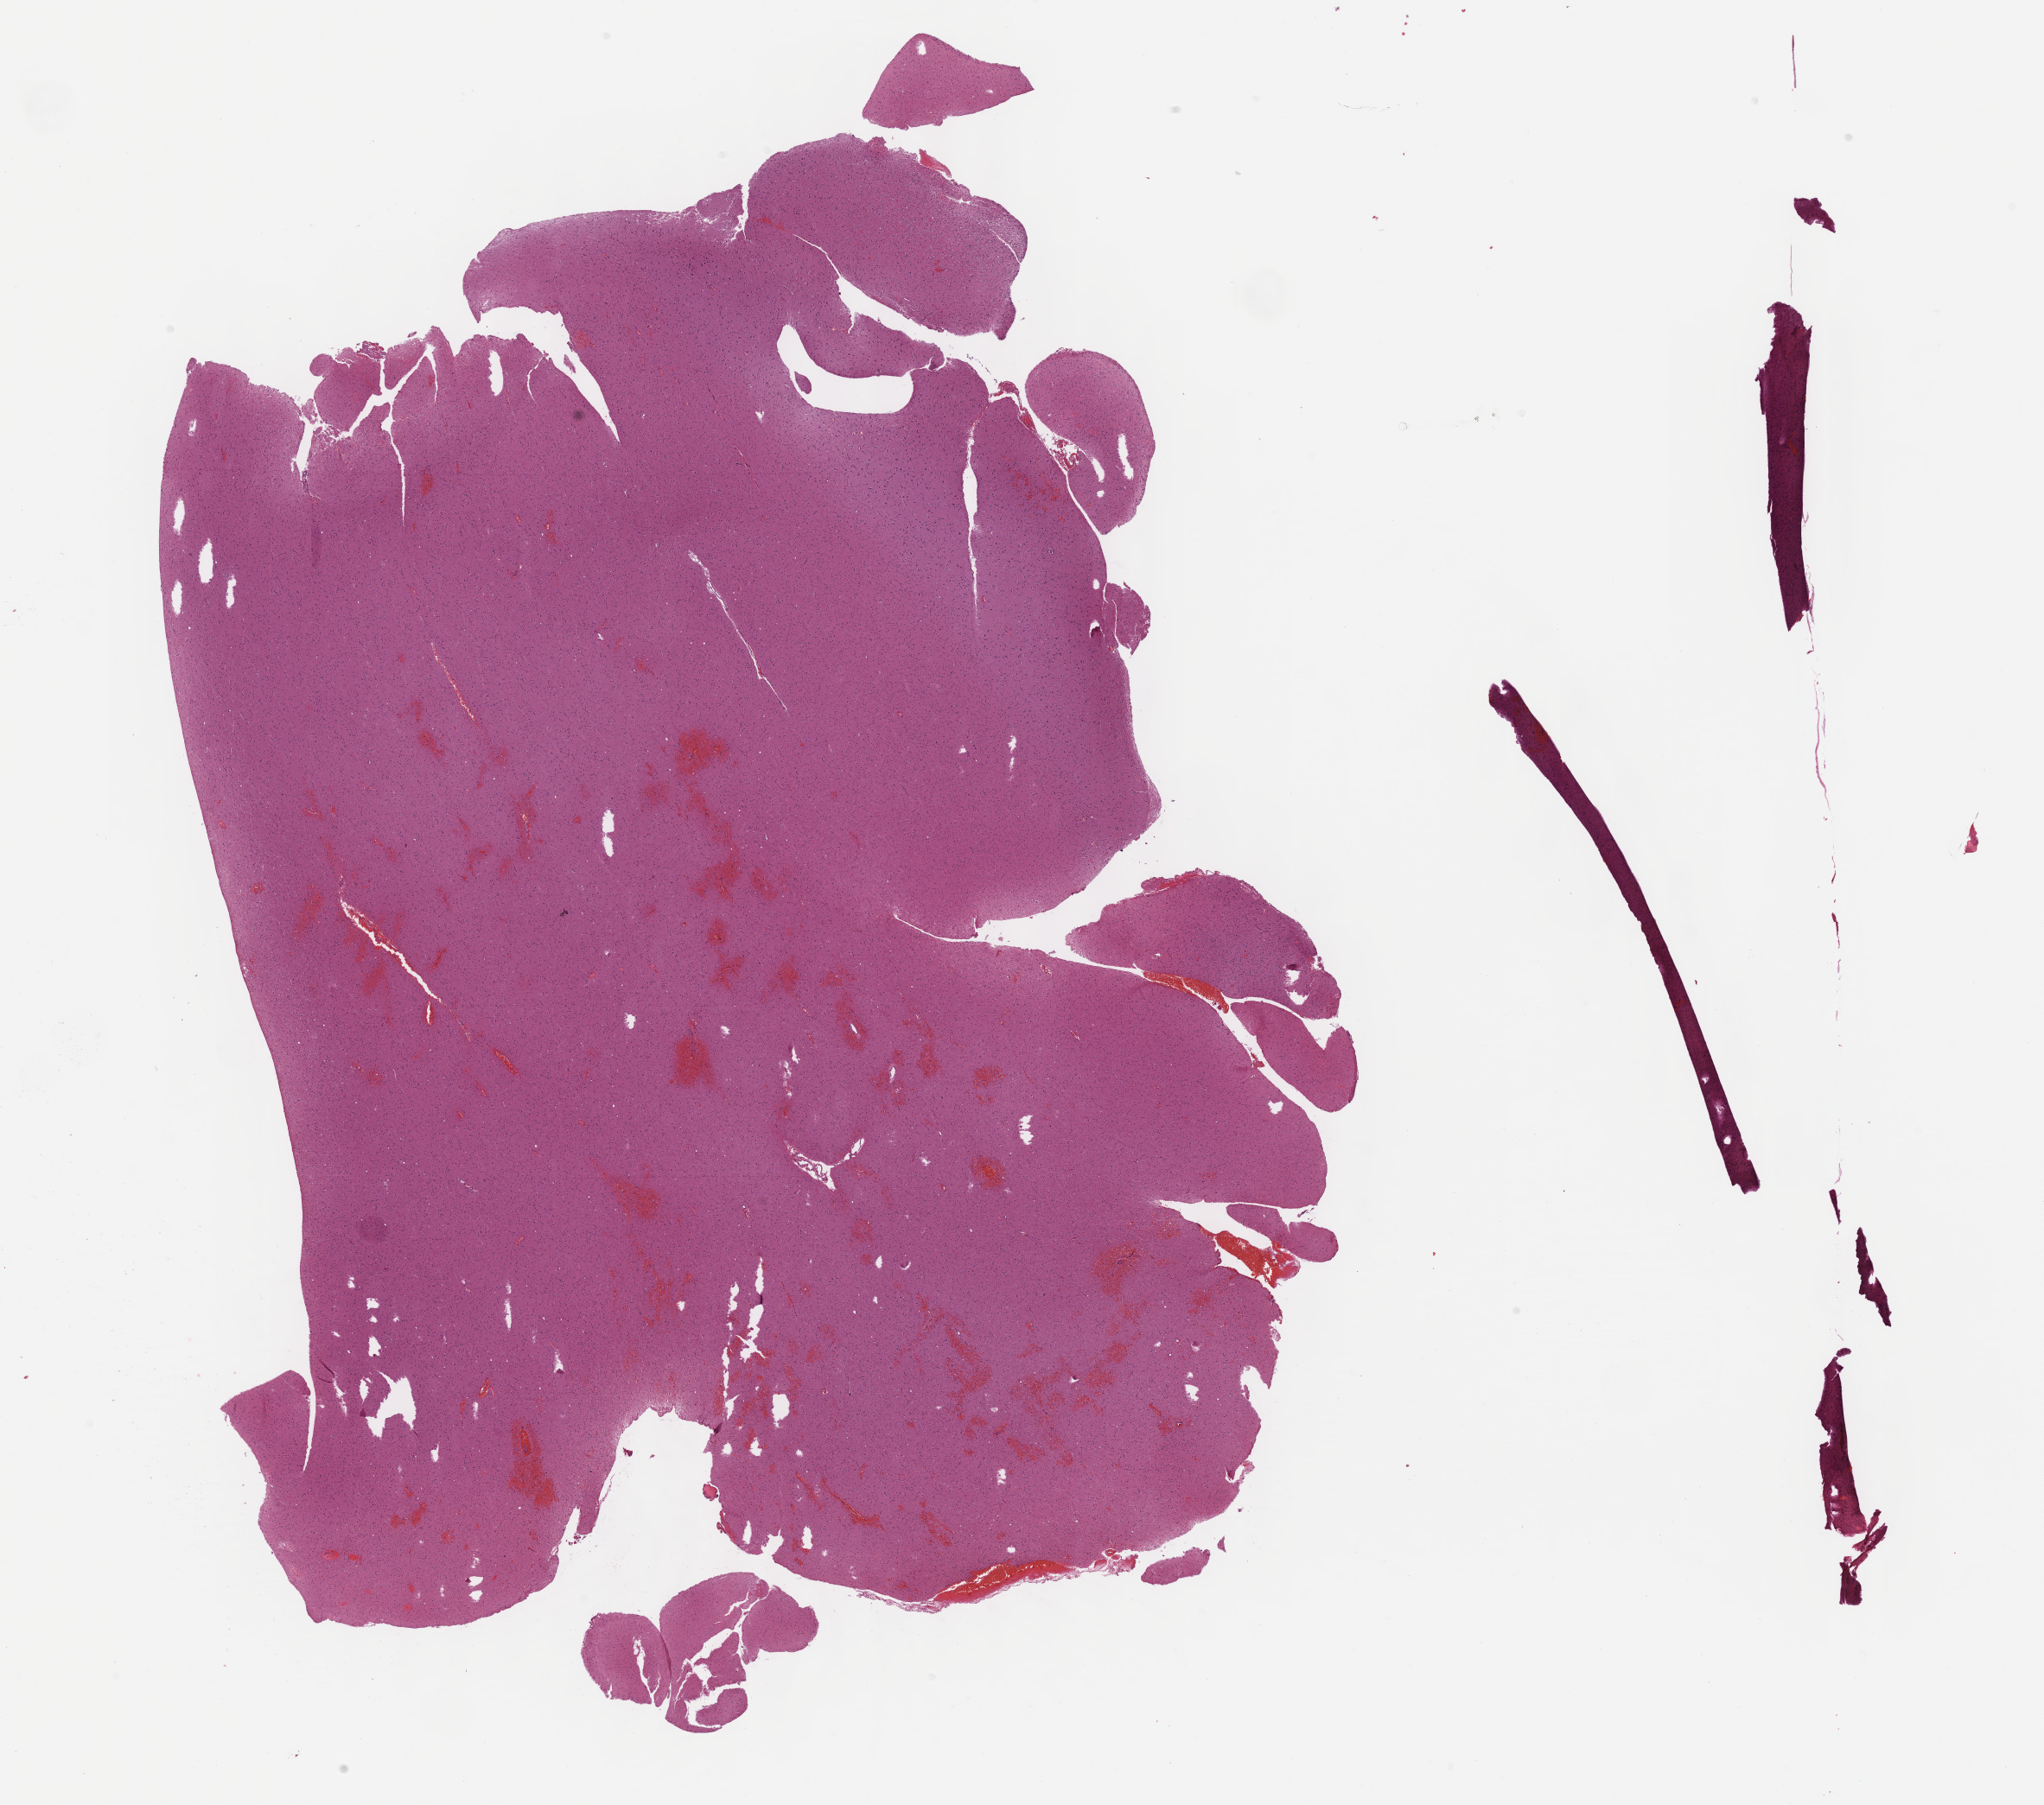
Whole-slide histology image, H&E-stained — a low-resolution overview of the entire scanned area, about 19.1 x 16.9 mm, FFPE section, primary tumour sample from the brain. Male, age 40 years at initial diagnosis. Histologic grade: G3 (poorly differentiated).
- diagnosis: Oligodendroglioma, anaplastic